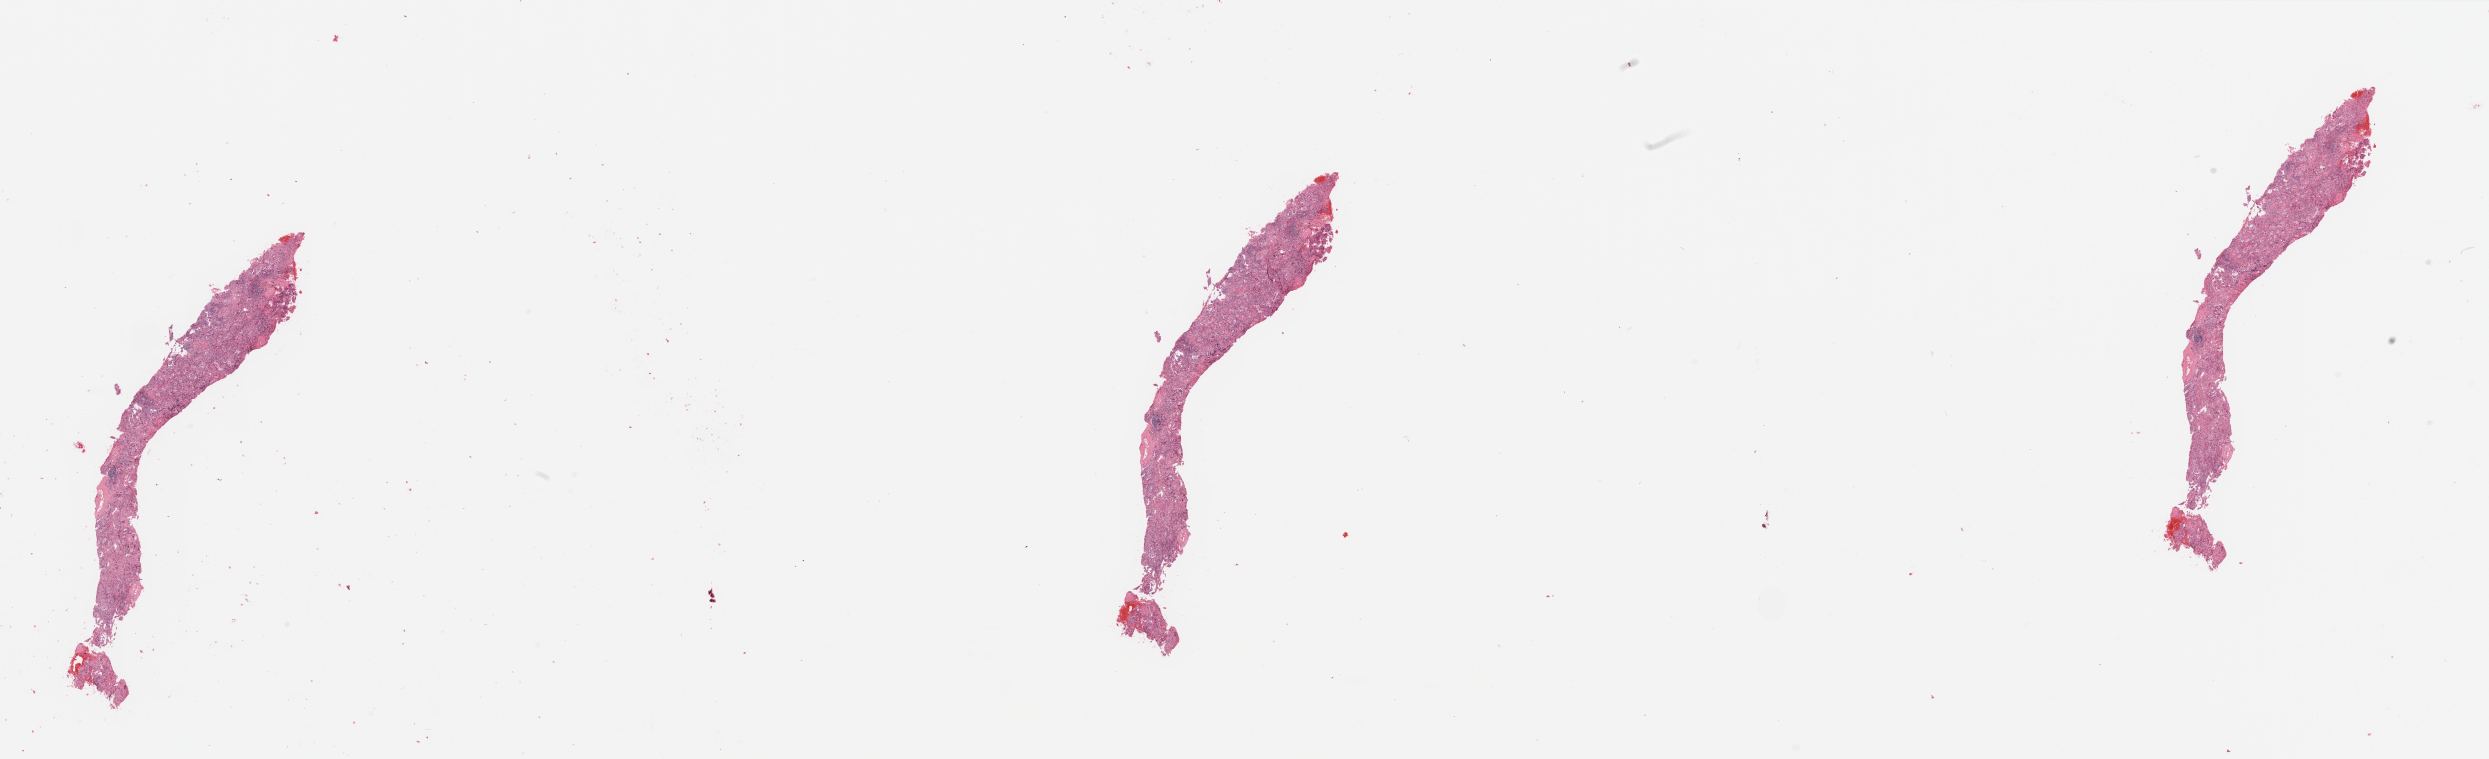
H&E-stained whole-slide image, low-resolution overview of the scanned area, about 39.4 x 12.0 mm; tumour tissue sample, lung. 81-year-old male patient. Histologic grade: G2 (moderately differentiated).
- AJCC pathologic stage: IIA
- diagnosis: Adenocarcinoma, NOS
- primary tumour site (as recorded): right lower lobe